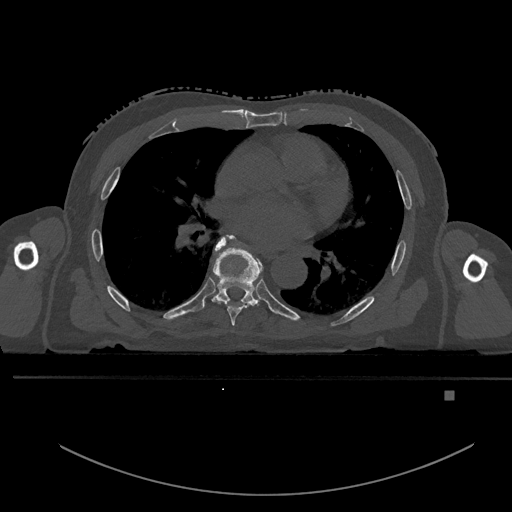
CT including the spine, one axial slice. Slice 279 of 969 in the series (ordered by position). Bone window (W 1800 / L 400 HU). 0.5 mm slice thickness. 512 × 512 image matrix. Male patient, age 82 years. From the clinical record (not read from this slice): primary cancer: prostate; vertebrae with lytic lesions (as recorded): T11, T9, T8, T2.
Outlined on this slice (semi-automatically segmented with operator editing):
- T6 vertebra: box from (x=214, y=235) to (x=251, y=326) px
- T7 vertebra: (x=212, y=236)–(x=262, y=306)